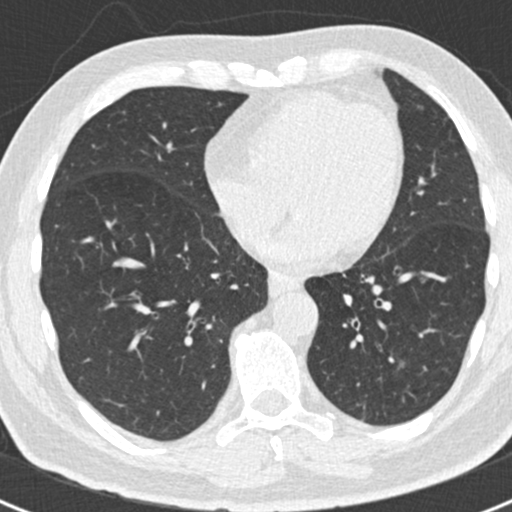
Chest CT (low-dose screening protocol), one axial image; first (baseline) screen; lung window (W 1500 / L -600 HU); 2 mm slice thickness; standard (soft-tissue) reconstruction kernel (B30f); 120 kVp; 512 × 512 image matrix. Male participant, aged 66 years at enrolment. Former smoker at enrolment.
- Lesion marked by an expert reader, box from (x=340, y=335) to (x=420, y=413) px.
- Screening reader's record for this exam (one nodule recorded; not confirmed to be the boxed lesion): non-calcified nodule or mass ≥4 mm, left lower lobe, 43 × 27 mm, smooth margins.
- Participant outcome: lung cancer diagnosed 801 days after this screen (after the third annual screen) — adenocarcinoma, NOS, left lower lobe, poorly differentiated (G3), stage IB (AJCC 6th edition), 38 mm at pathology.